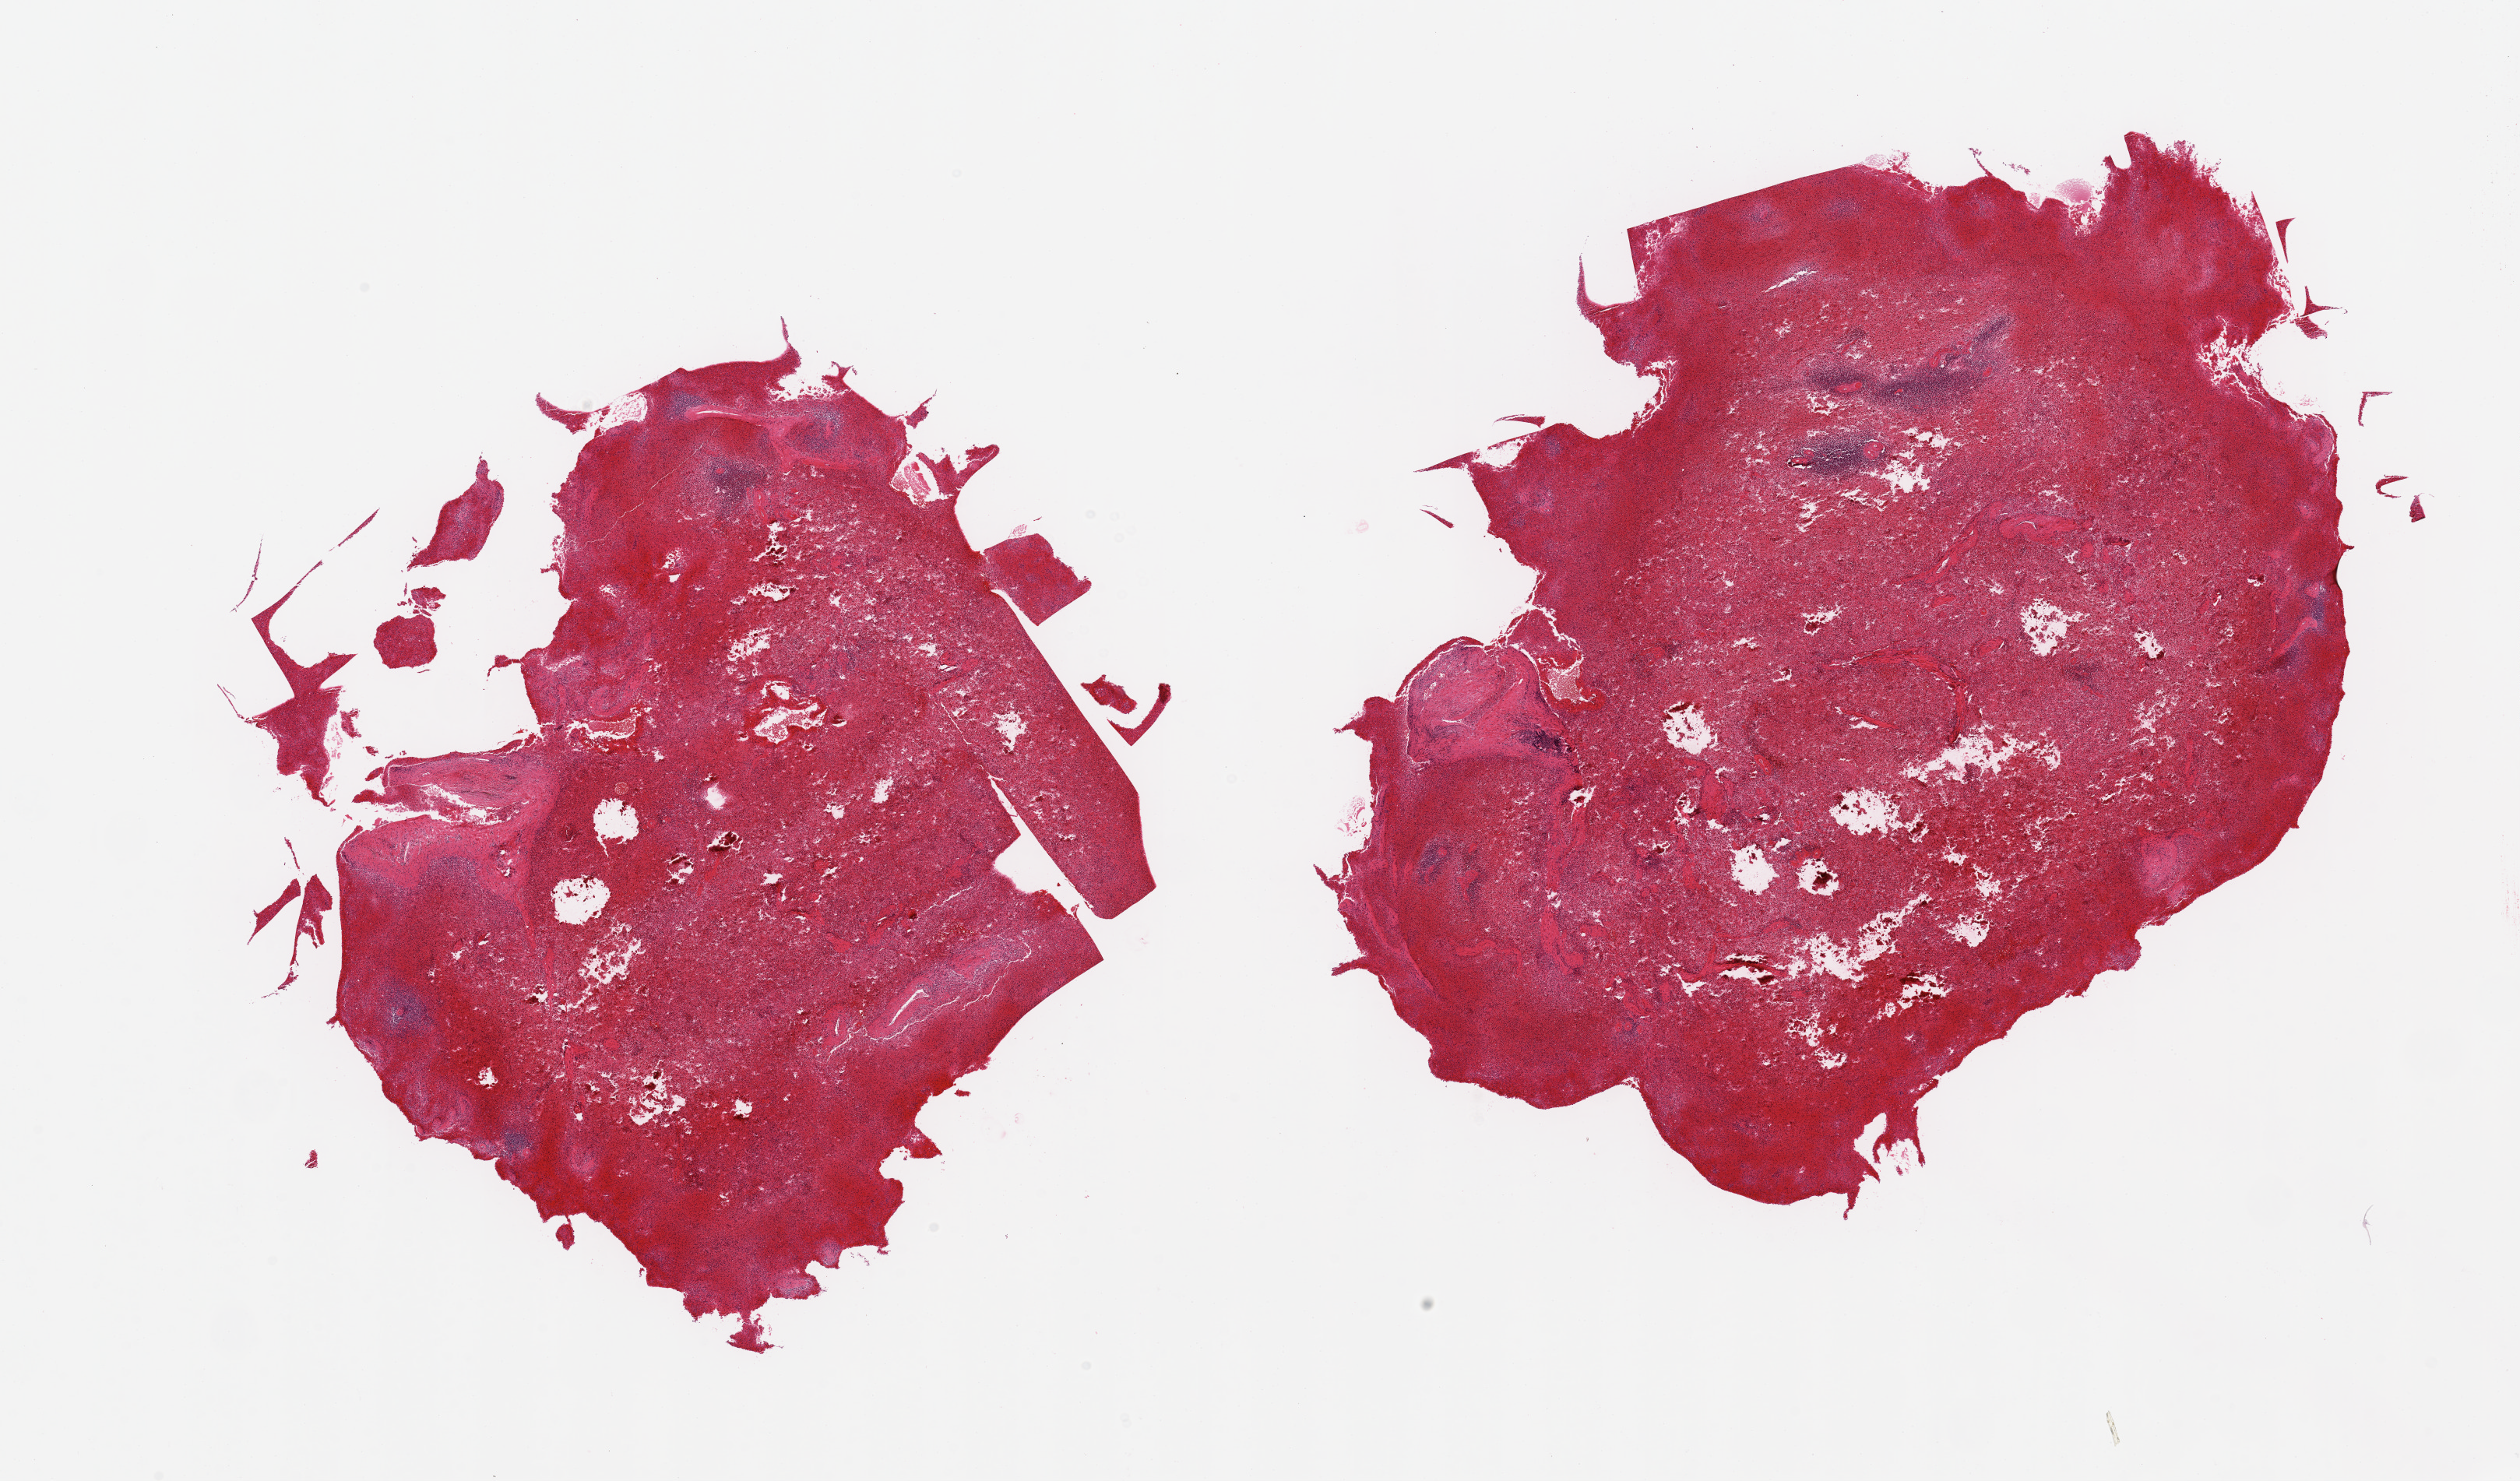
H&E whole-slide image — shown as a low-resolution overview of the whole scanned area (about 25.6 x 15.0 mm), PAXgene-fixed paraffin-embedded (PFPE) section, section of spleen (target tissue), donor tissue sample. Donor: male.
Reviewer comment on this tissue sample: 2 pieces; severe congestion.